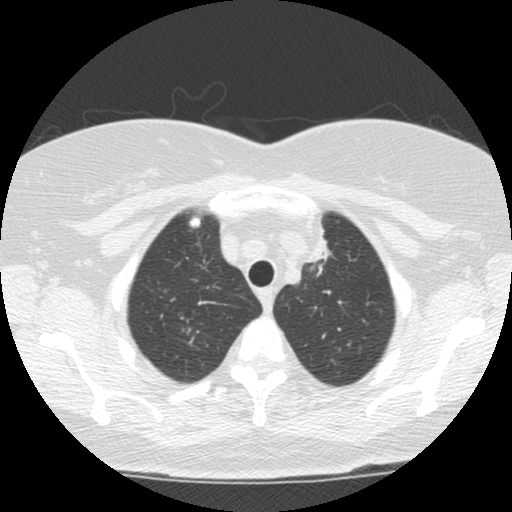
Low-dose screening chest CT, one axial slice. Slice 99 of 120 in the series (ordered by position). Reconstruction kernel STANDARD. 120 kVp. Lung window (W 1500 / L -600 HU). 2.5 mm slice thickness. 512 × 512 image matrix, field of view 310 × 310 mm.
Annotated regions visible in this slice (manually delineated by an expert):
- lesion 1 (tumor, upper lobe of left lung): bounding box [x1, y1, x2, y2] px = [307, 229, 331, 263]